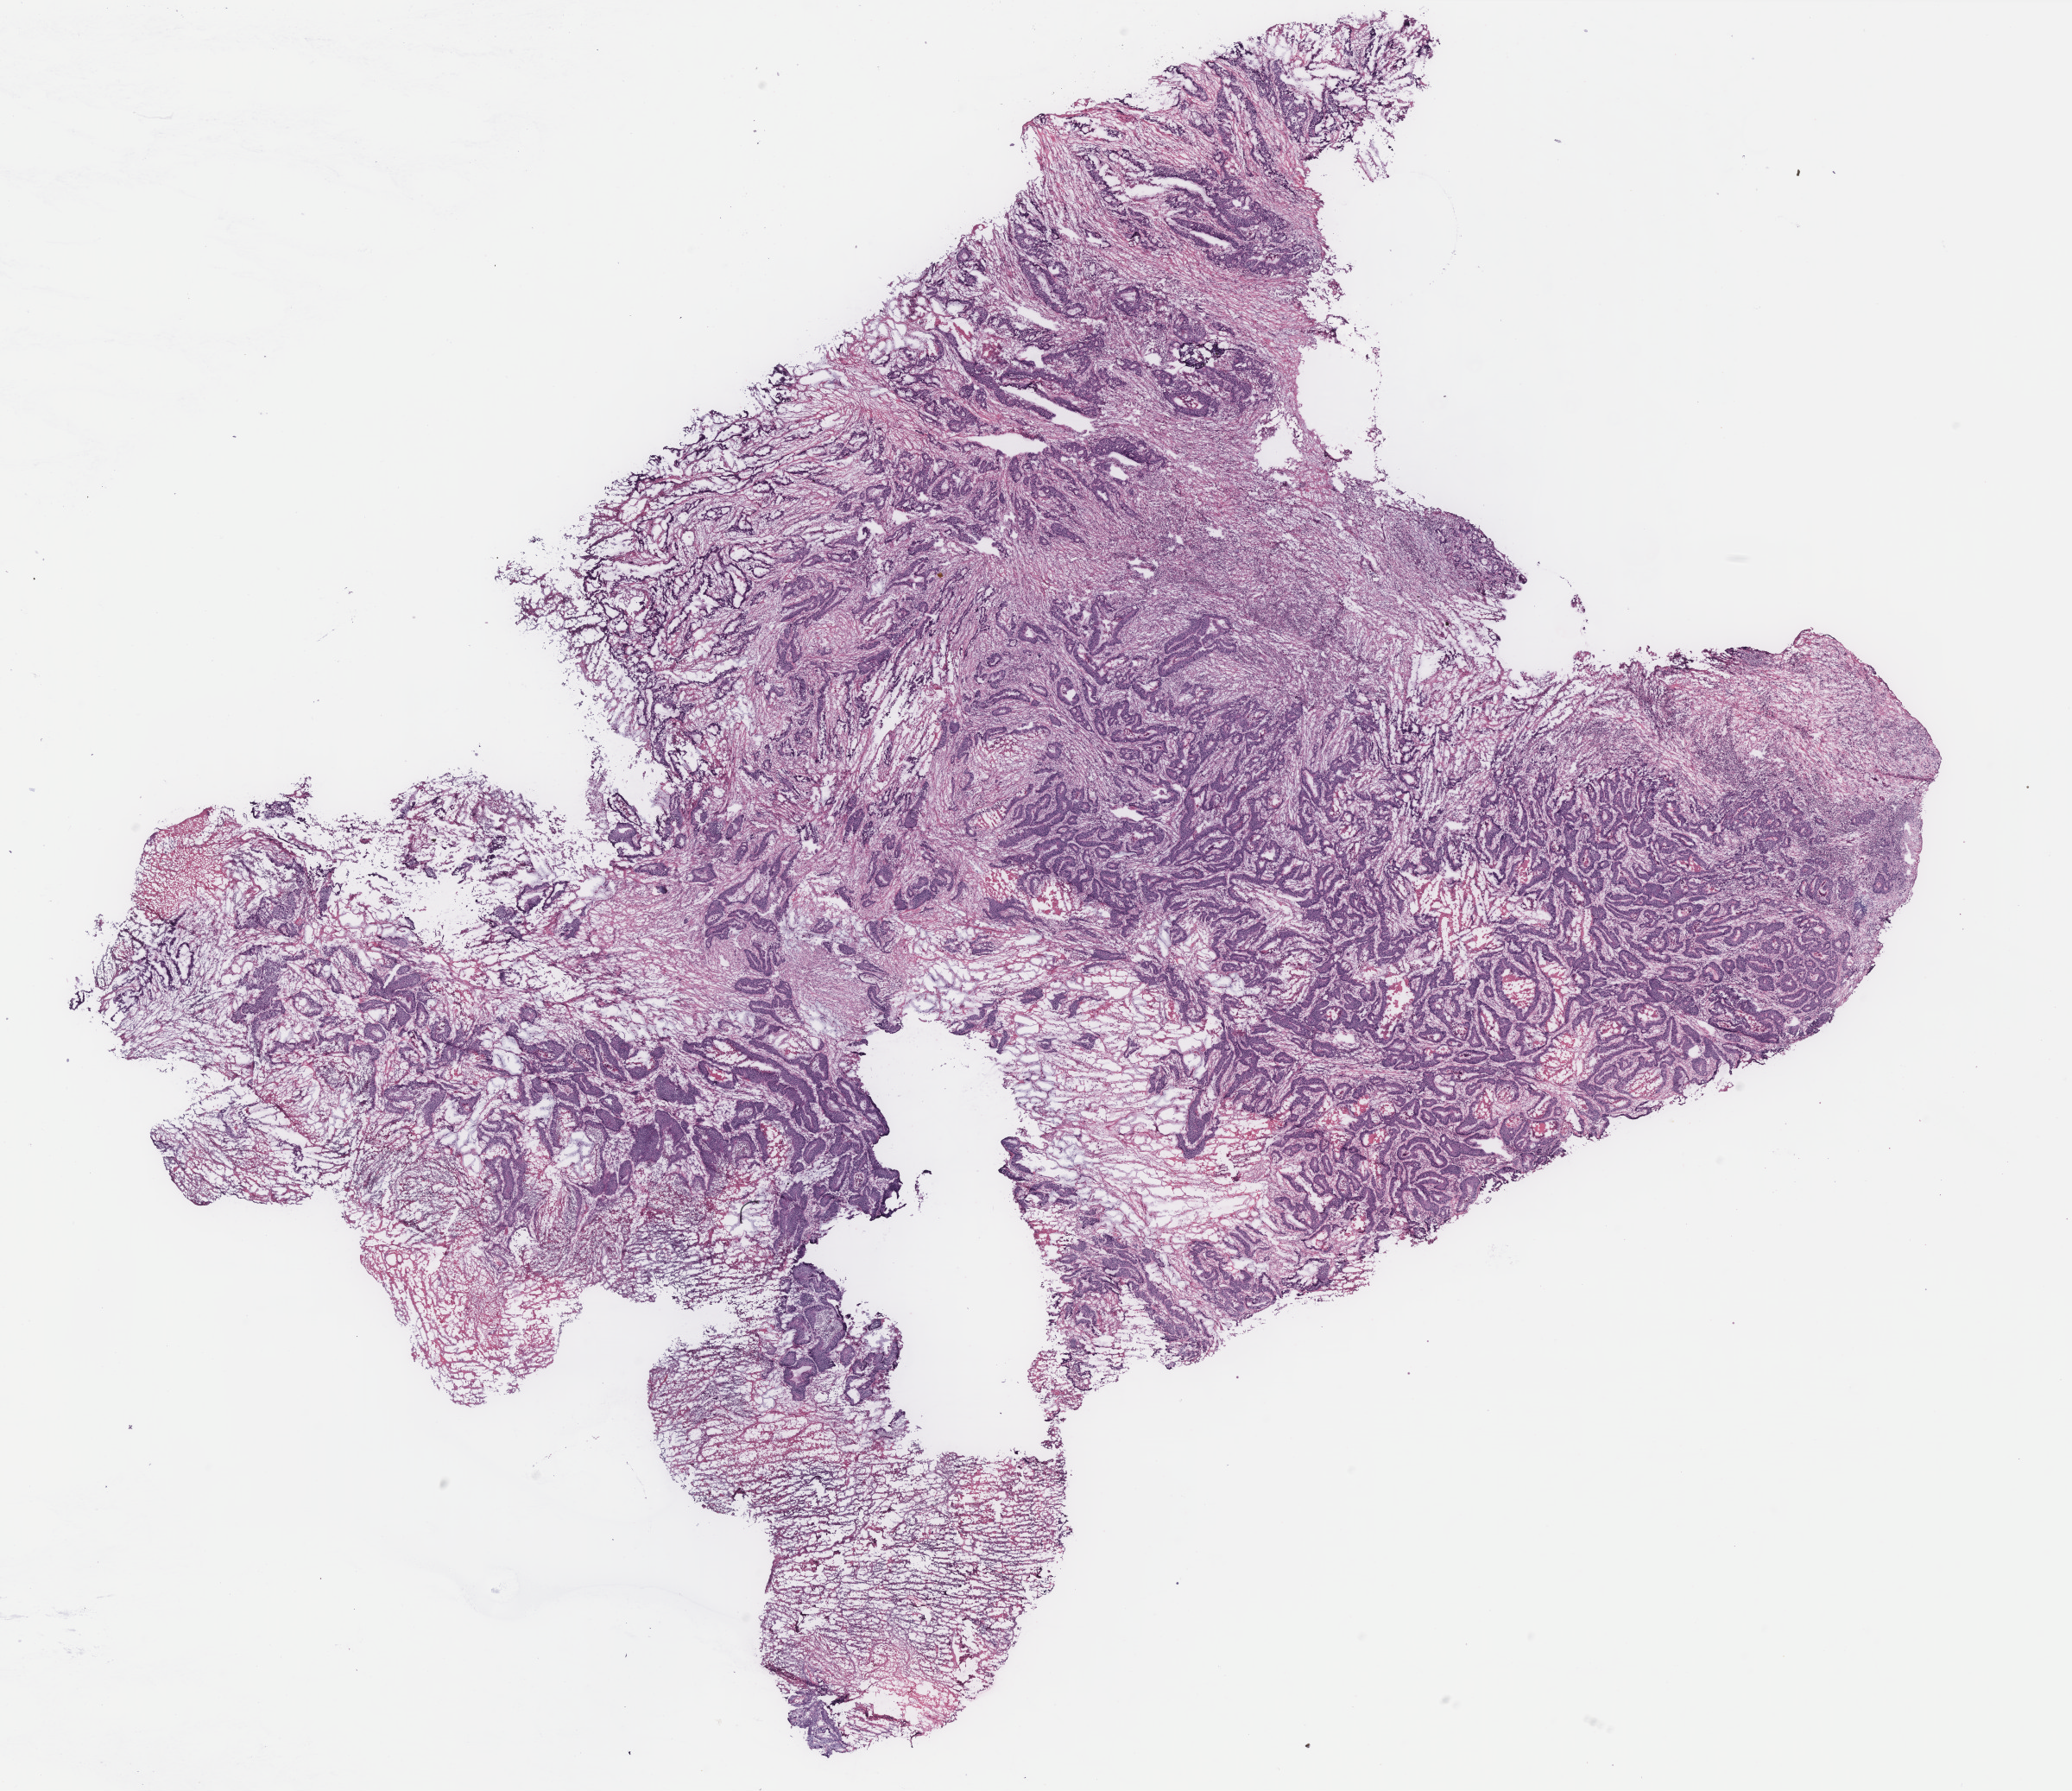
Whole-slide histology image, Hematoxylin and eosin (H&E) stained, shown as a low-resolution overview of the whole scanned area (about 19.2 x 16.6 mm, from a 40x scan); colon, tissue type not recorded.
Patient diagnosis (cohort enrolment): colon cancer (colon).